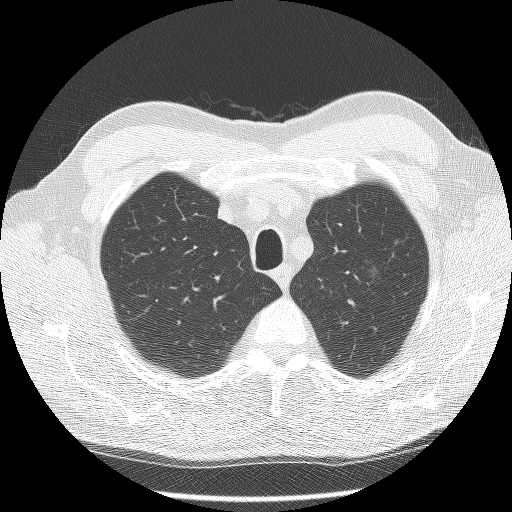
Low-dose screening chest CT, axial slice, second annual screen, lung window (W 1500 / L -600 HU), 2.5 mm slice thickness, 120 kVp, slice 23 of 124 in the series. Male, age 60 years at enrolment. Former smoker at enrolment.
• Lesion marked by an expert reader, bounding box [x1, y1, x2, y2] px = [352, 253, 403, 297].
• The screening reader recorded 2 non-calcified nodules or masses ≥4 mm on this exam; which of them this box marks is not recorded.
• Official screen result: positive, no significant change: stable abnormalities potentially related to lung cancer, unchanged since the prior screening exam.
• Lung cancer was diagnosed 448 days after this screen: bronchiolo-alveolar carcinoma, non-mucinous, left upper lobe, well differentiated (G1), stage IA (AJCC 6th edition), 16 mm at pathology.